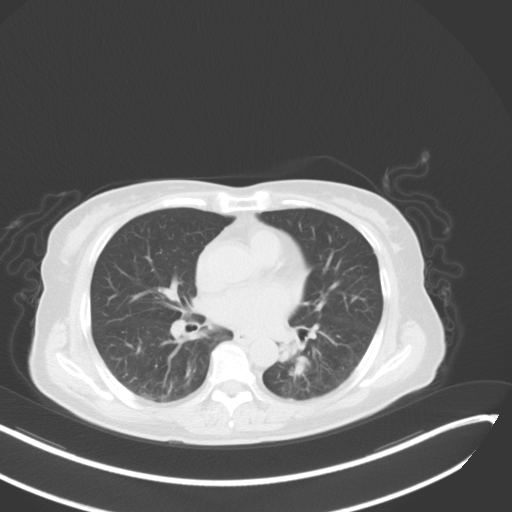
Chest CT, one axial slice; position 18 of 48 along the scan axis; lung window (W 1500 / L -600 HU); 512 × 512 image matrix, field of view 400 × 400 mm. Patient: female, 64 years. Case-level facts recorded for this patient, not image findings: clinical TNM (as recorded): T3 N1 M1.
Annotated regions visible in this slice (bounding box drawn by a radiologist):
- lung tumour (recorded histology: small cell carcinoma): bounding box [x1, y1, x2, y2] px = [274, 330, 309, 375]